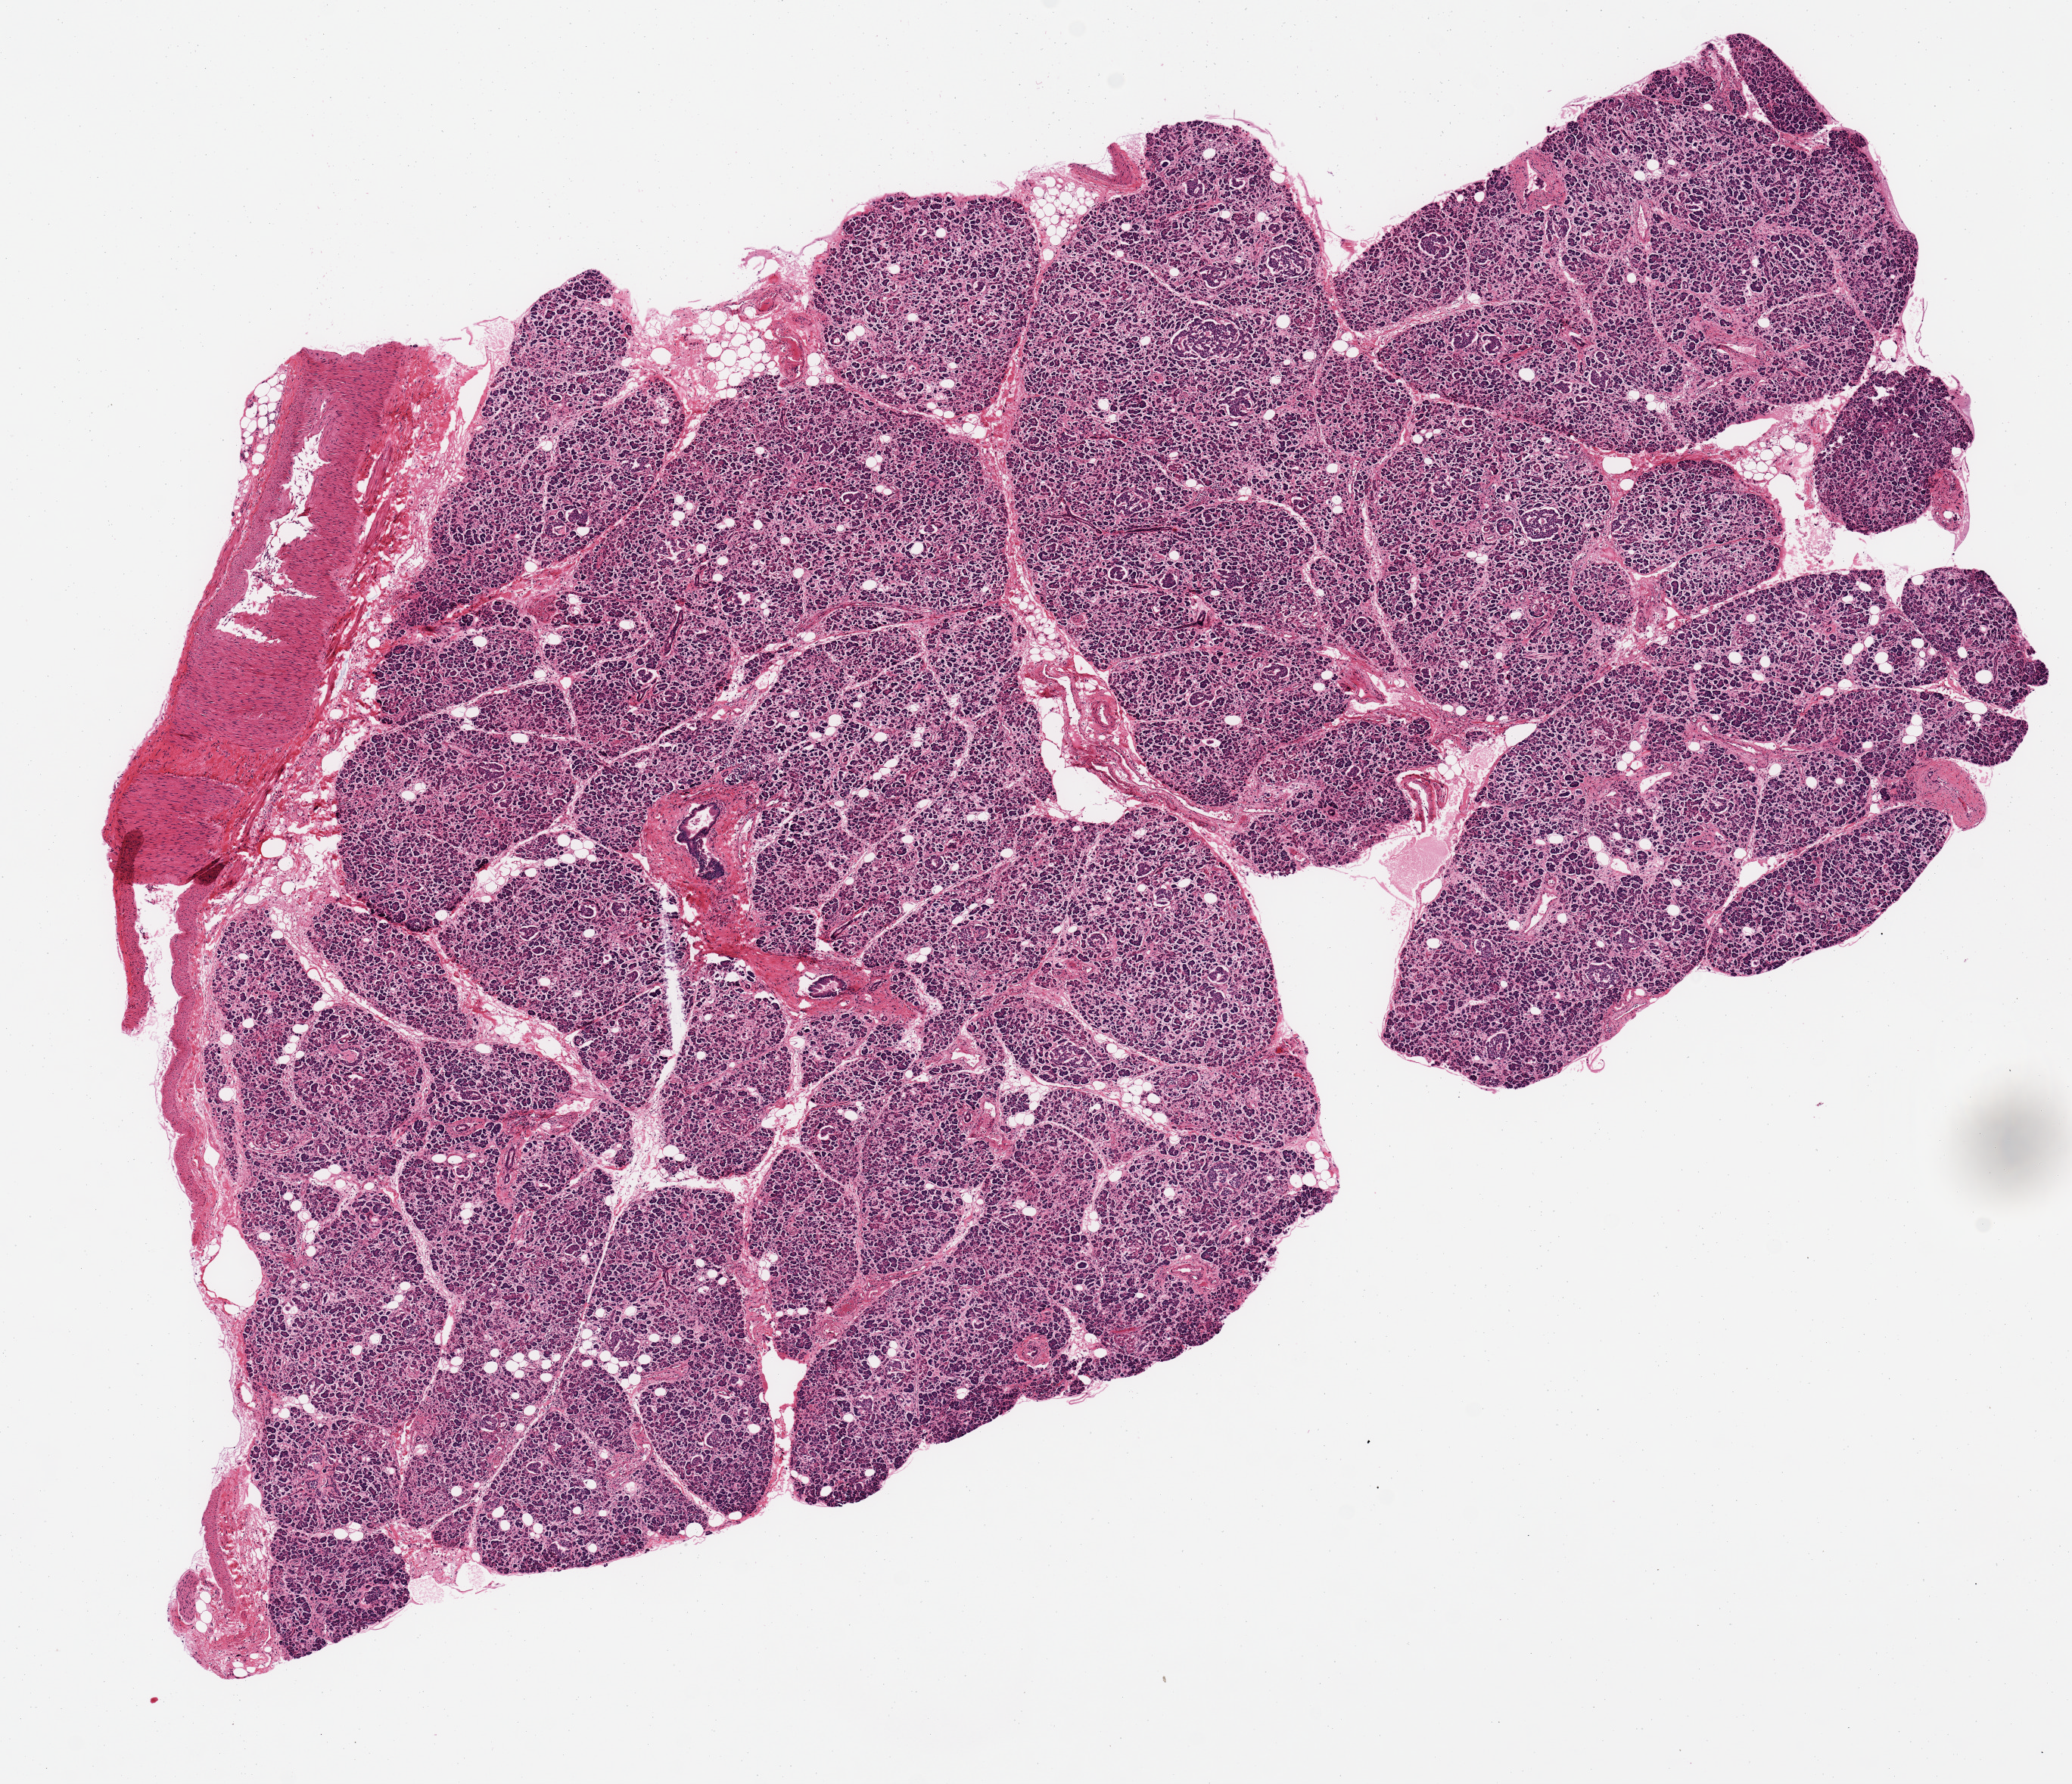
Haematoxylin and eosin whole-slide image, brightfield, a low-resolution overview of the entire scanned area, about 10.8 x 9.3 mm (acquisition: 20x scan), PAXgene-fixed paraffin-embedded (PFPE) section, target tissue: pancreas, donor tissue sample. Donor sex: female.
Pathologist's review note for this sample: Typical post mortem peripancreatic saponification. 2.8mm segment of small muscular artery appended to one edge of specimen.